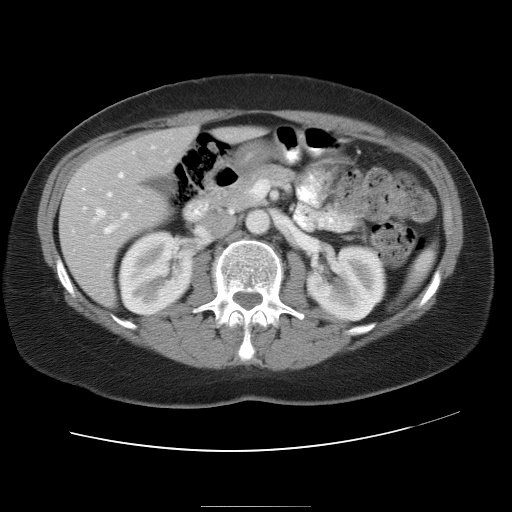
Contrast-enhanced abdominal CT, one axial slice; slice 15 of 30 in the series (ordered by position); reconstruction kernel STANDARD; 120 kVp; intravenous contrast given; soft-tissue window (W 400 / L 40 HU); 7.5 mm slice thickness; 512 × 512 image matrix. Female patient, age 52 years. Case-level facts recorded for this patient, not image findings: diagnosis: colorectal cancer liver metastases, imaged before liver resection; multiple liver metastases: no; largest metastasis: 3 cm; disease in both lobes: yes.
Structures marked on this image (expert manual segmentation):
- hepatic veins: box from (x=93, y=150) to (x=167, y=222) px
- liver: (x=59, y=127)–(x=255, y=304)
- planned liver remnant (the part of the liver to remain after resection): (x=162, y=127)–(x=258, y=157)
- portal vein (with intrahepatic branches): (x=104, y=173)–(x=140, y=234)